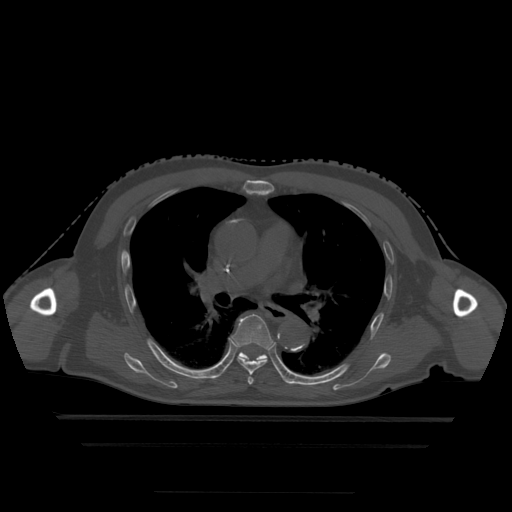
CT including the spine, one axial slice. Bone window (W 1800 / L 400 HU). 512 × 512 image matrix, field of view 436 × 436 mm. Patient age 68 years. From the clinical record (not read from this slice): primary cancer: urothelial.
Outlined on this slice (semi-automatic segmentation, software-assisted and operator-edited):
- T5 vertebra: bounding box [x1, y1, x2, y2] px = [248, 377, 254, 385]
- T6 vertebra: [232, 314, 273, 375]
- T7 vertebra: [226, 352, 283, 378]